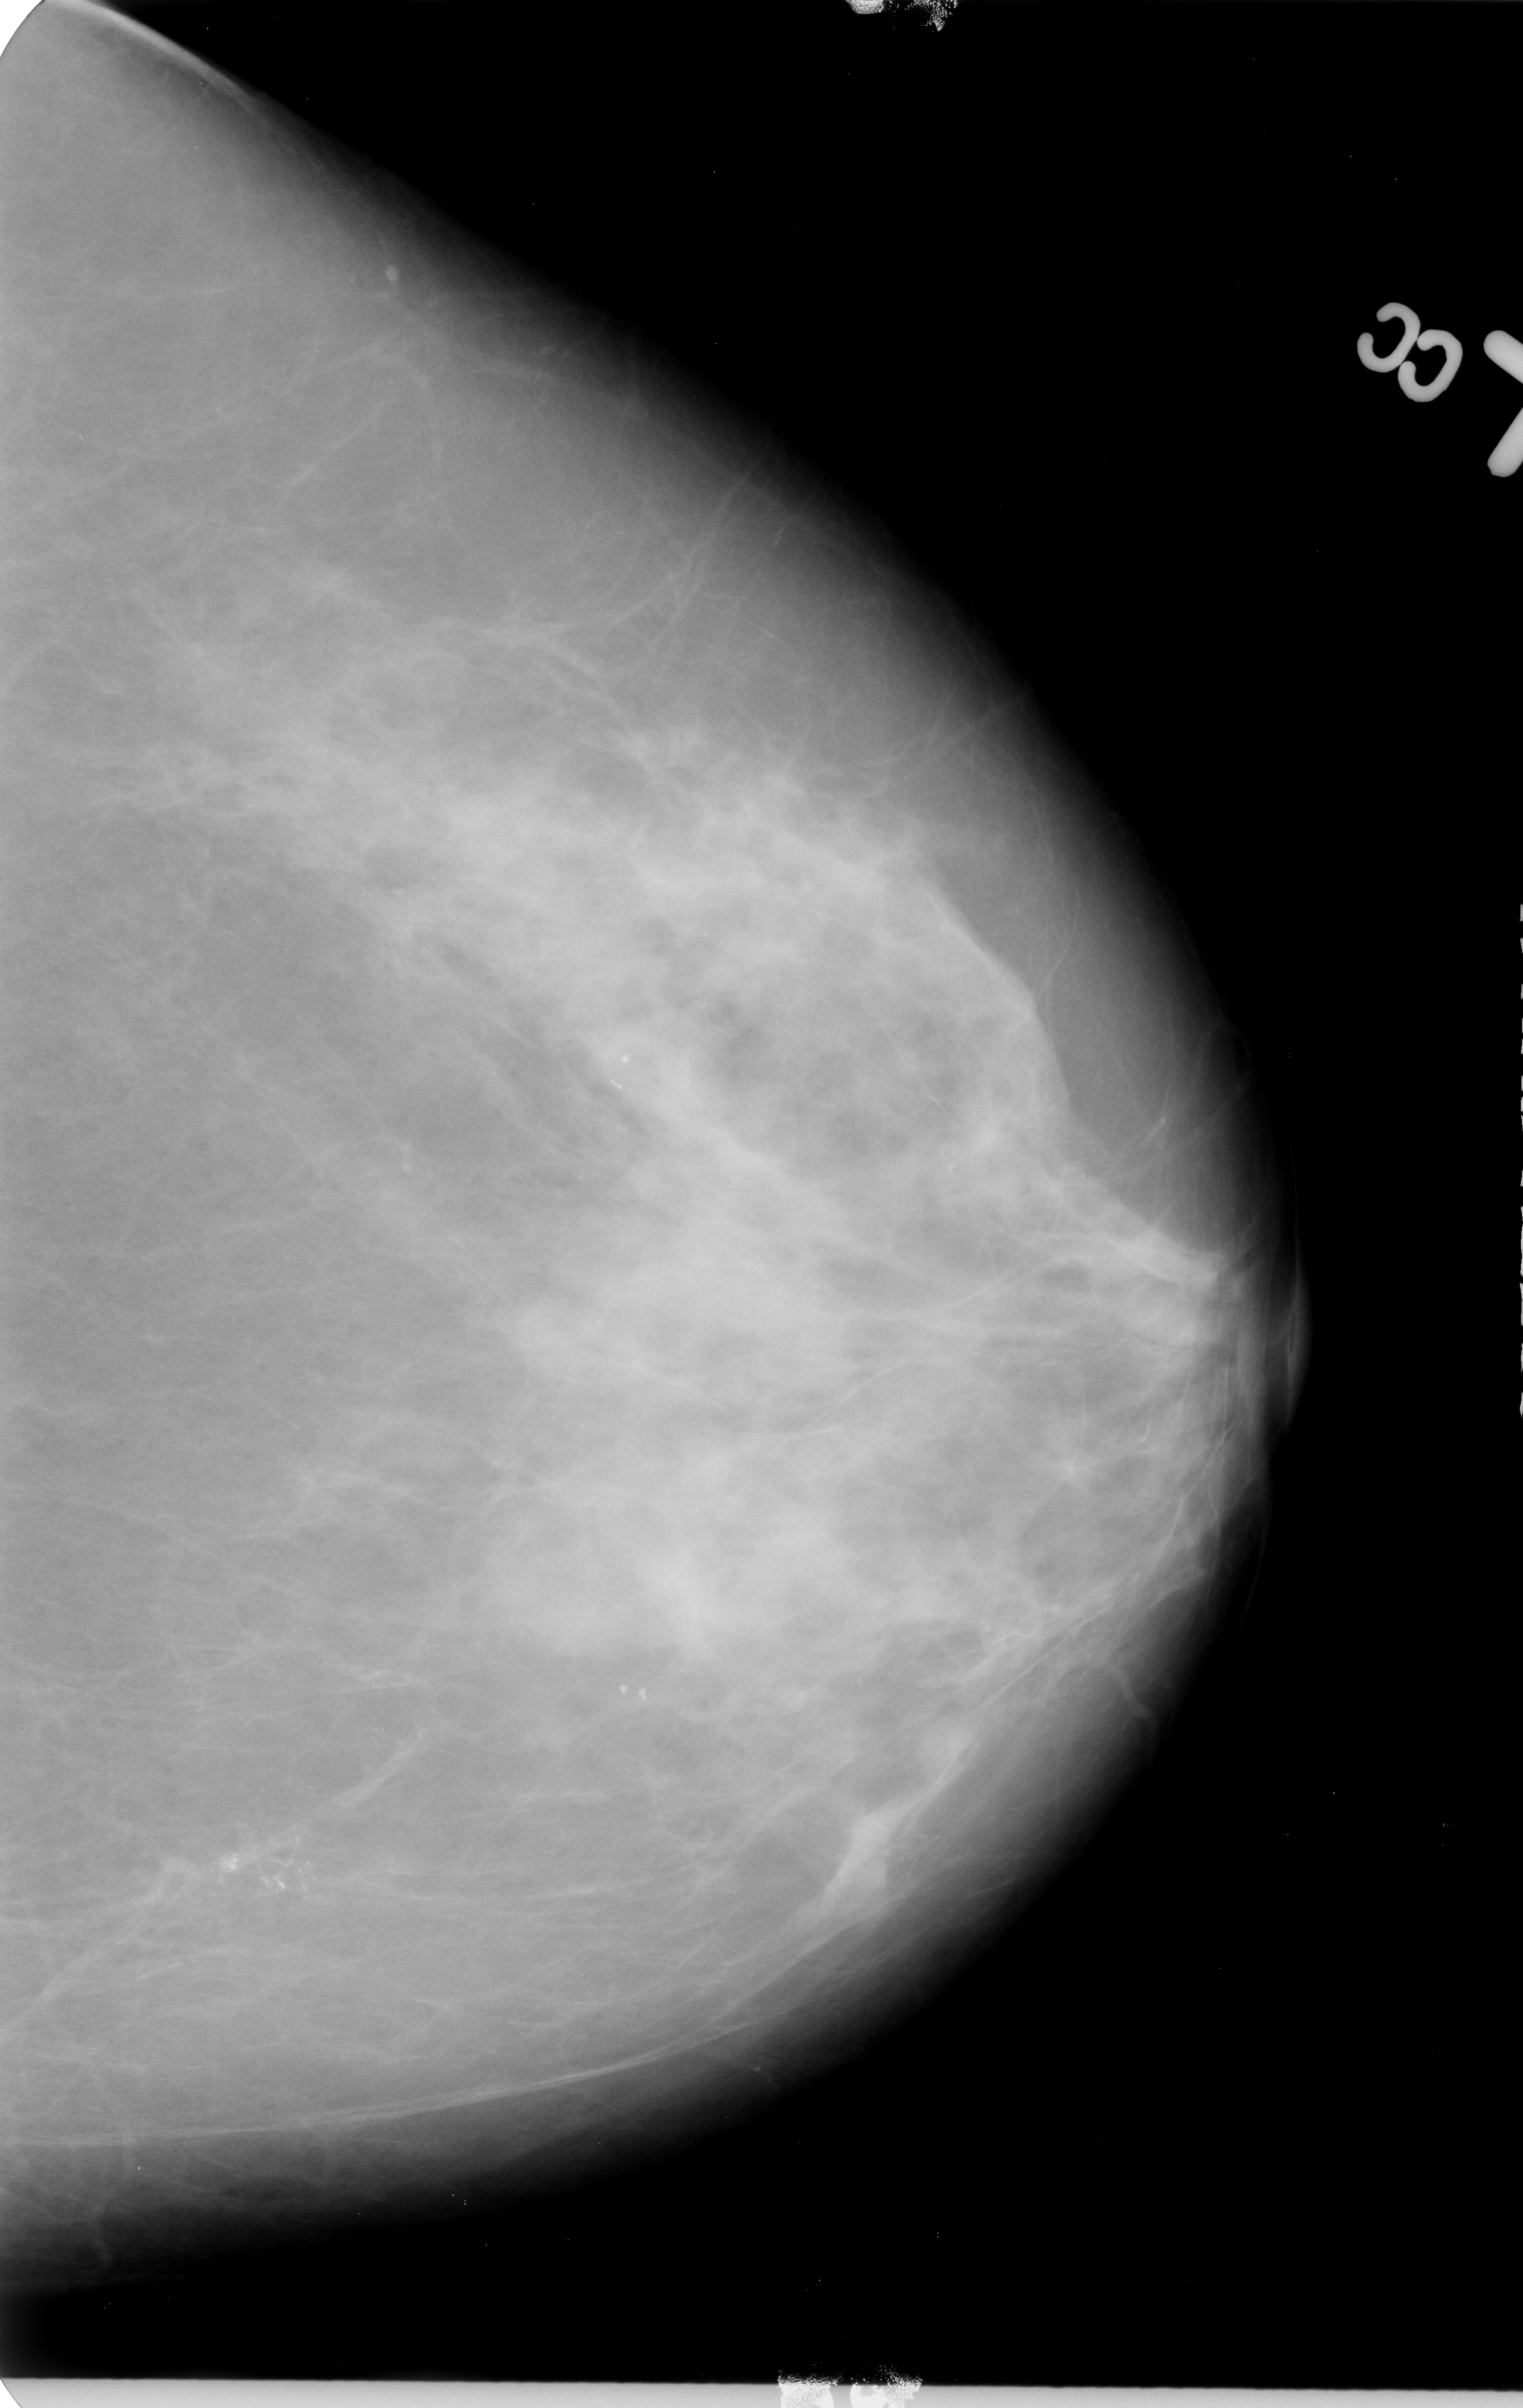
Scanned film-screen mammogram. Left breast. CC view. Breast composition: heterogeneously dense (BI-RADS density category 3 of 4). 1523 × 2408 image matrix.
Marked abnormalities (boxes around the expert regions of interest):
- calcifications, morphology pleomorphic / fine linear branching, distribution clustered / linear; BI-RADS assessment category 5; subtlety rating 4 on a 1 (subtle) to 5 (obvious) scale; pathology (as recorded): malignant: bounding box <160,1778,376,1956> (left, top, right, bottom; pixels)